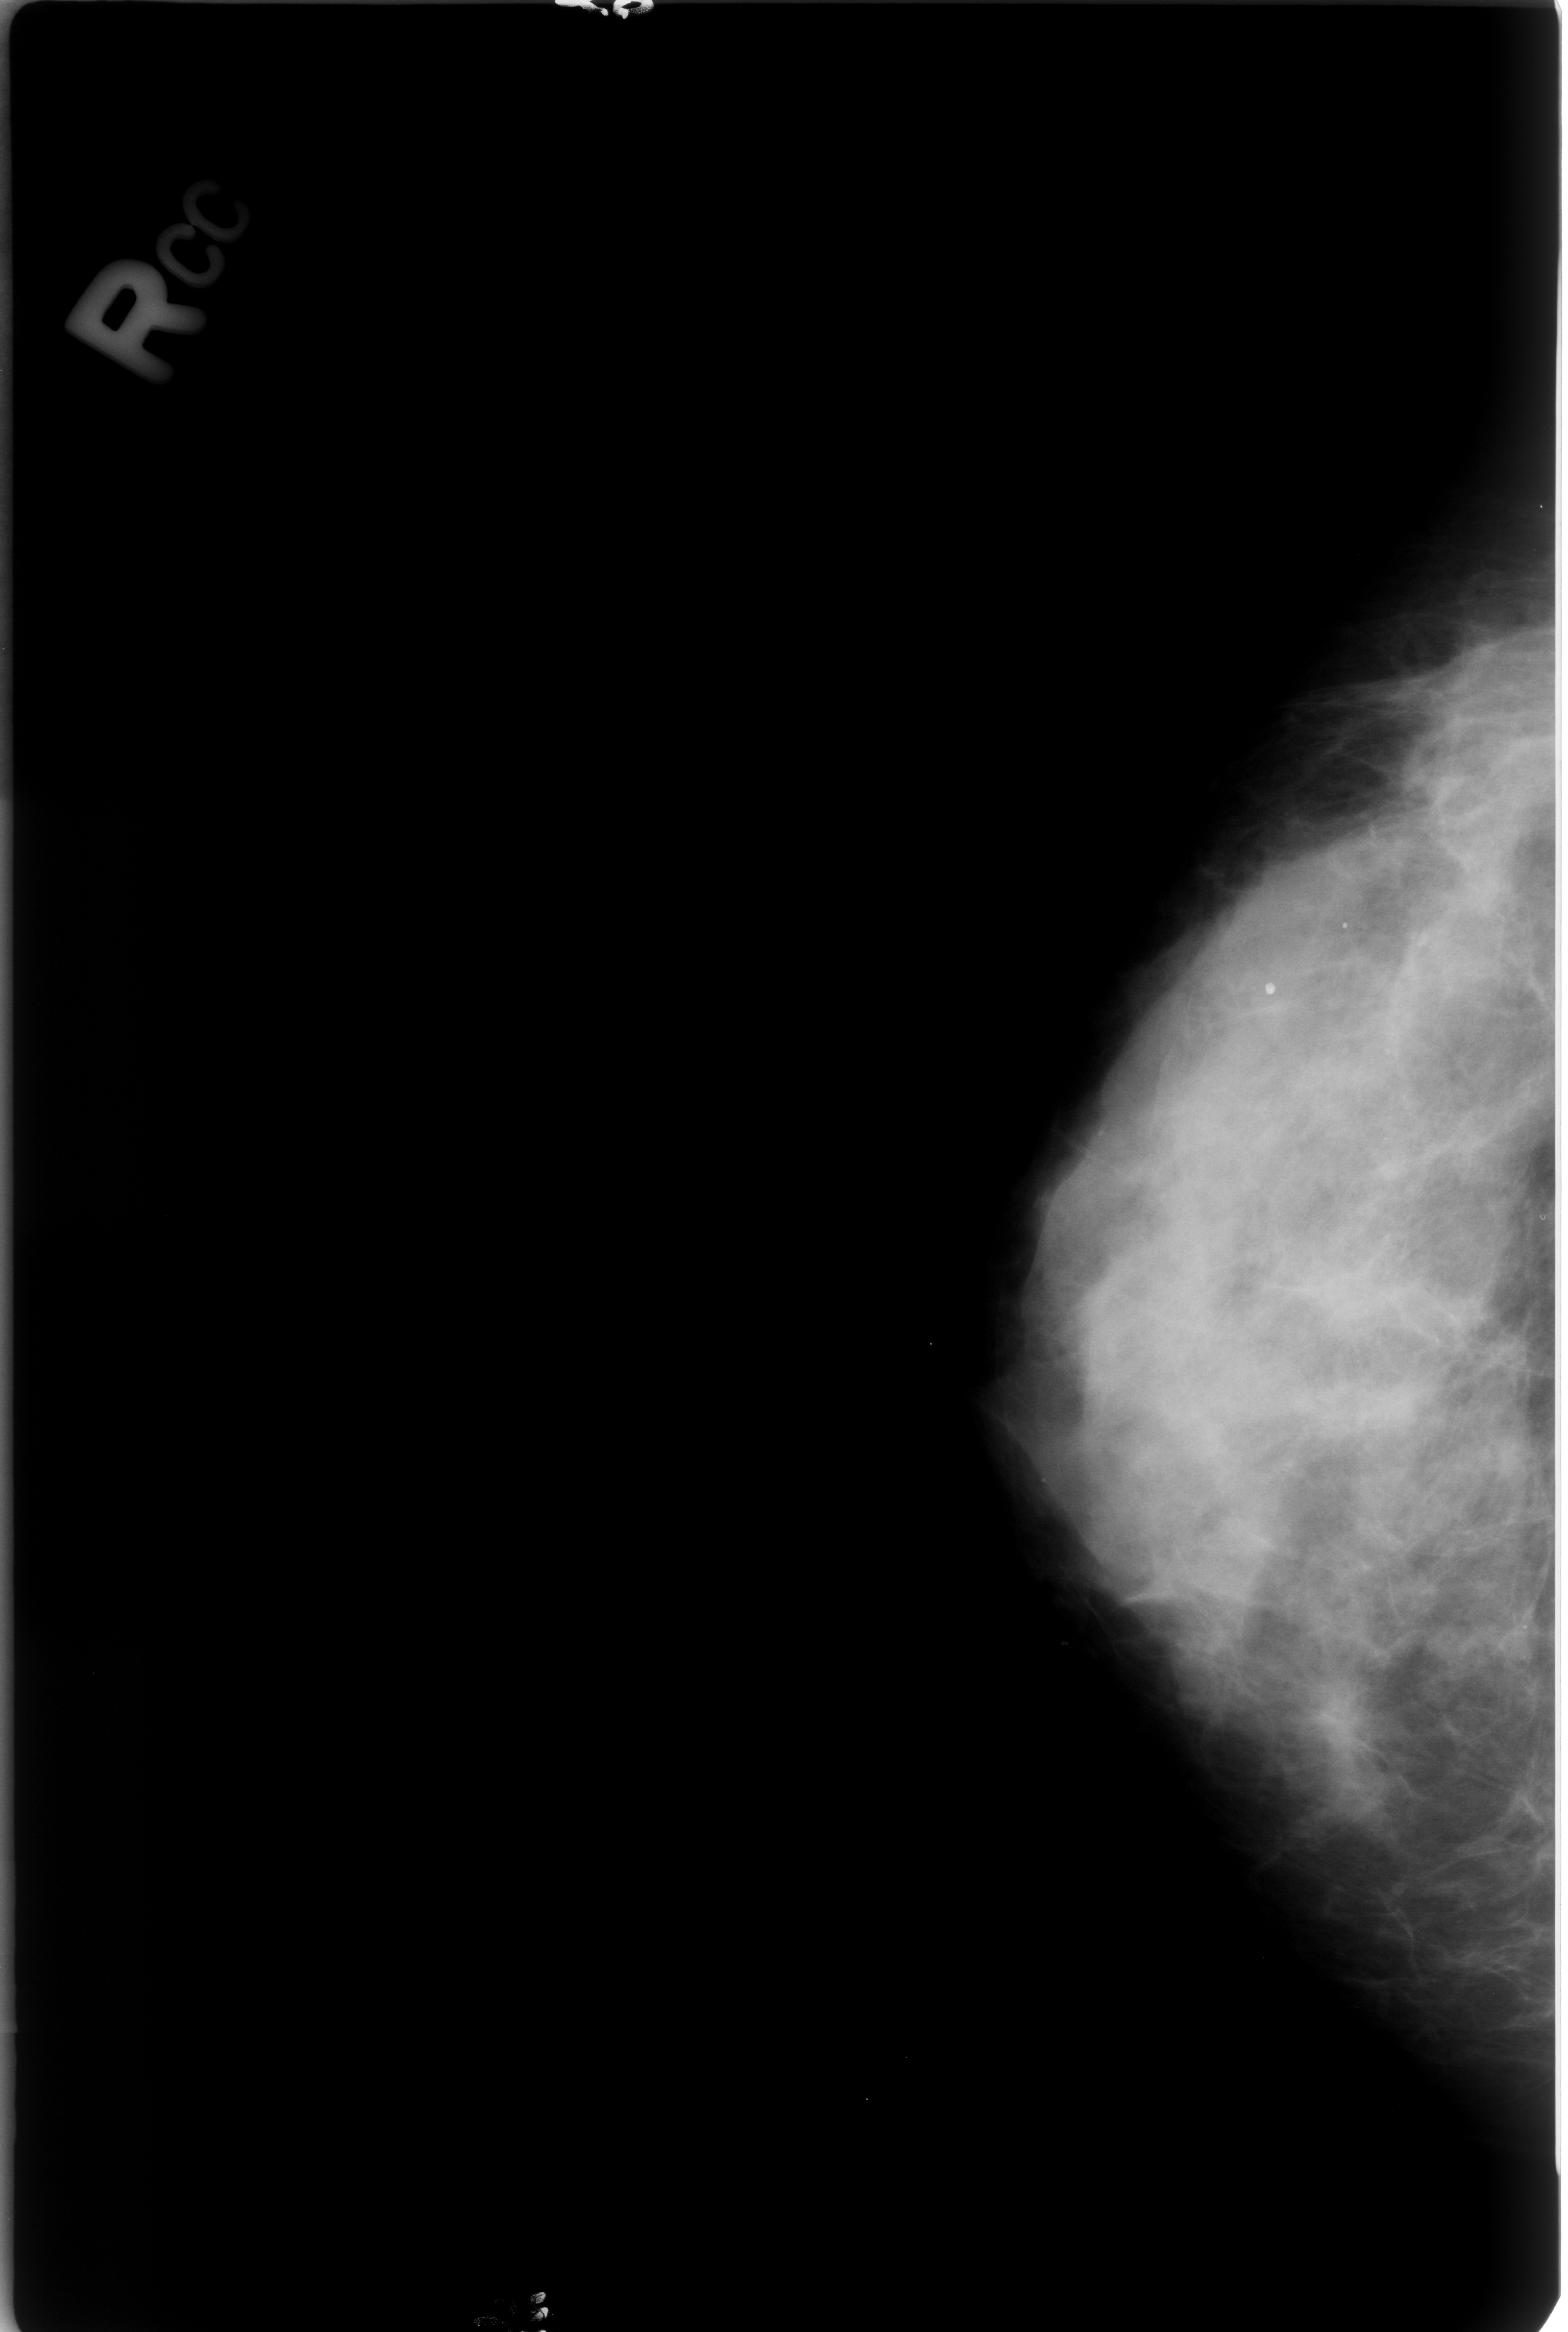
Mammogram (digitized film). Right breast. Craniocaudal (CC) view. Breast composition: heterogeneously dense (BI-RADS density category 3 of 4). 1568 × 2332 image matrix.
Marked abnormalities (boxes around the expert regions of interest):
- Finding 1 of 2: calcifications, morphology round and regular / lucent center; BI-RADS assessment category 2; subtlety rating 4 on a 1 (subtle) to 5 (obvious) scale; outcome (as recorded, no biopsy): benign without callback (not worked up further): bounding box <1257,980,1279,1002> (left, top, right, bottom; pixels)
- Finding 2 of 2: calcifications, morphology round and regular / lucent center; BI-RADS assessment category 2; outcome (as recorded, no biopsy): benign without callback (not worked up further): <1331,910,1353,940>